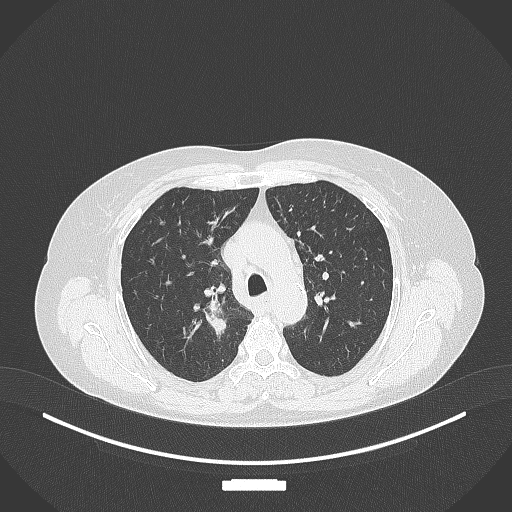
Chest CT, one axial slice. Position 269 of 357 along the scan axis. Reconstruction kernel B70f. Lung window (W 1500 / L -600 HU). 1 mm slice thickness. 512 × 512 image matrix. Patient: female, 62 years. Case-level facts recorded for this patient, not image findings: clinical TNM (as recorded): T1c N1 M0.
Structures marked on this image (rectangle marked by the reading radiologist):
- lung tumour (recorded histology: squamous cell carcinoma): bounding box <194,298,229,346> (left, top, right, bottom; pixels)